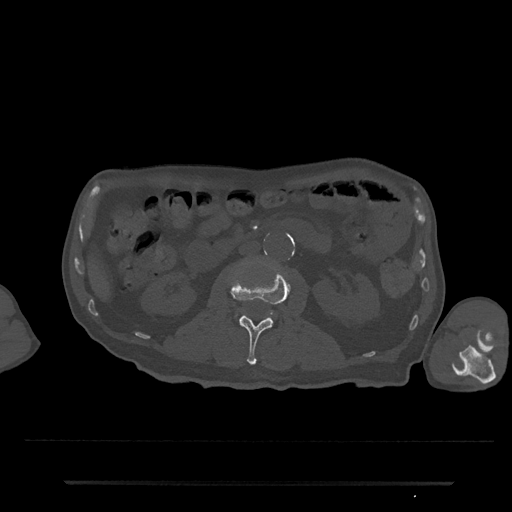
CT including the spine, one axial slice. Position 39 of 797 along the scan axis. Reconstruction kernel Br40s/3. 120 kVp. Bone window (W 1800 / L 400 HU). 512 × 512 image matrix. Male patient, age 74 years. From the clinical record (not read from this slice): primary cancer: prostate.
Structures marked on this image (semi-automatically segmented with operator editing):
- L2 vertebra: bounding box [x1, y1, x2, y2] px = [230, 267, 291, 365]
- L3 vertebra: [234, 308, 277, 317]